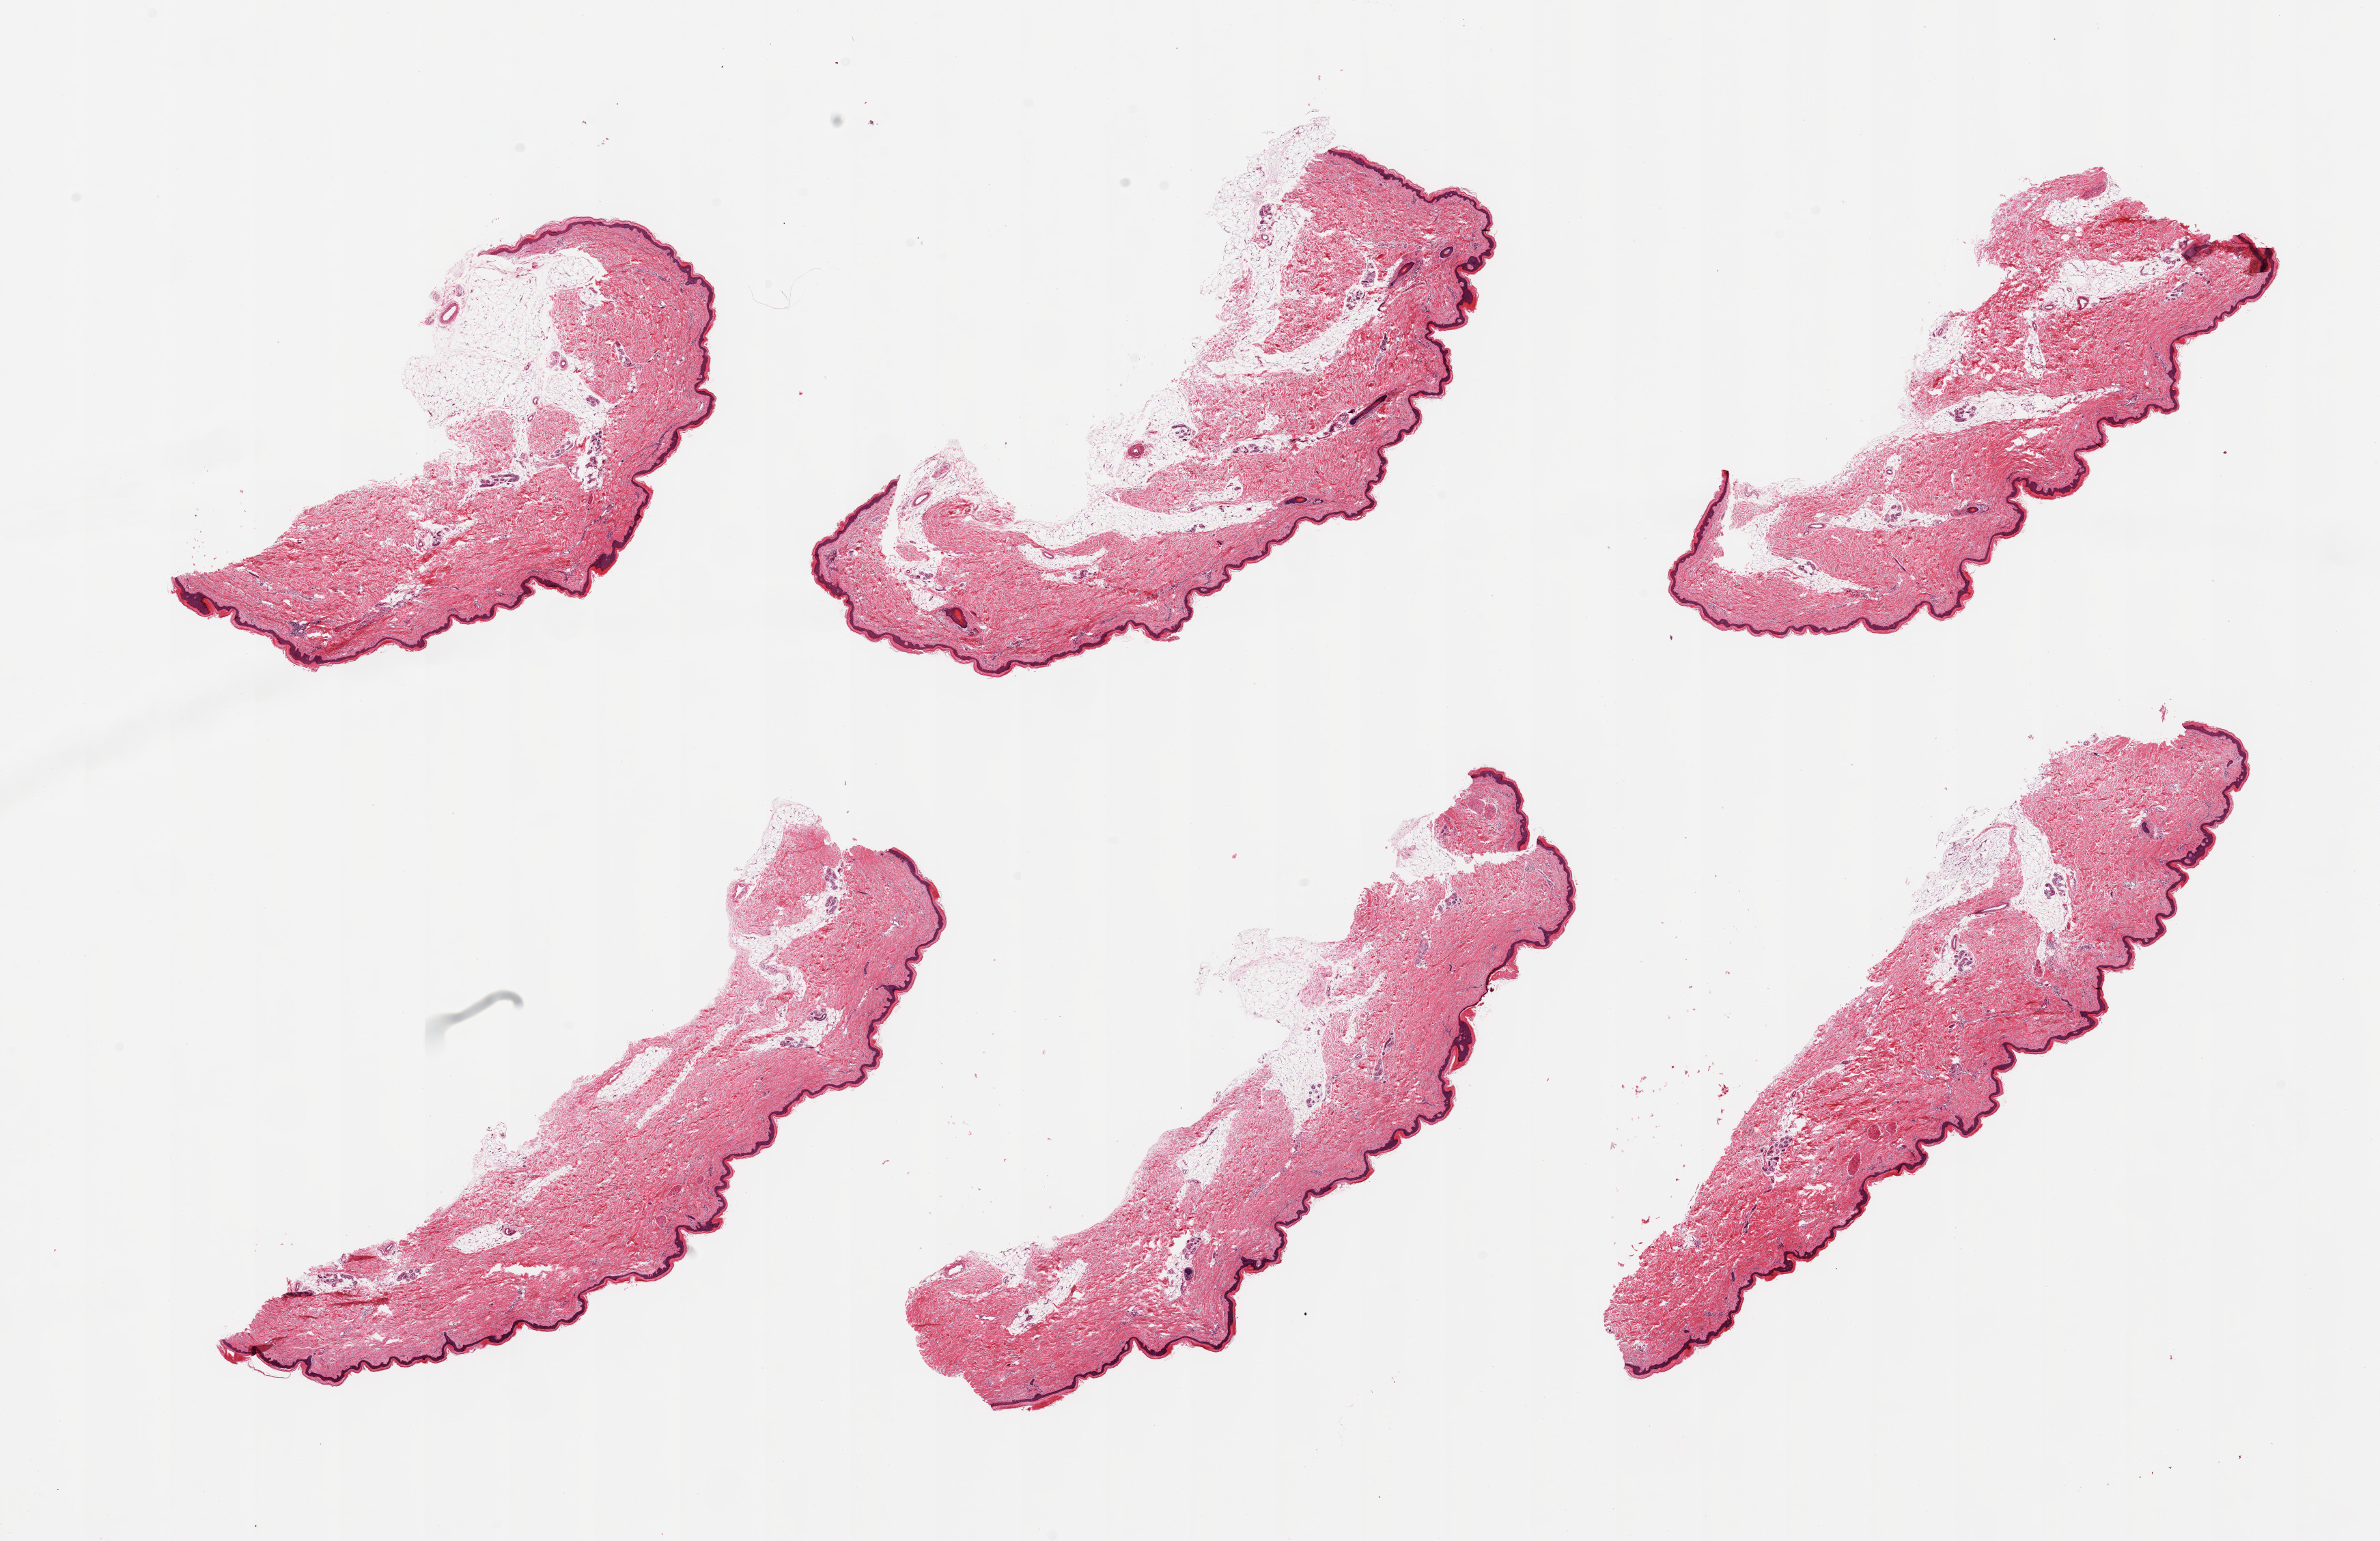
Haematoxylin and eosin whole-slide image, brightfield, whole scanned area (about 27.6 x 17.9 mm) shown as a low-resolution overview. PAXgene-fixed paraffin-embedded (PFPE) section. Target tissue: skin of lower leg. Tissue donor sample. Donor: female.
* pathologist's review note for this sample: 6 pieces few foci adherent fat ~0.5-1mm